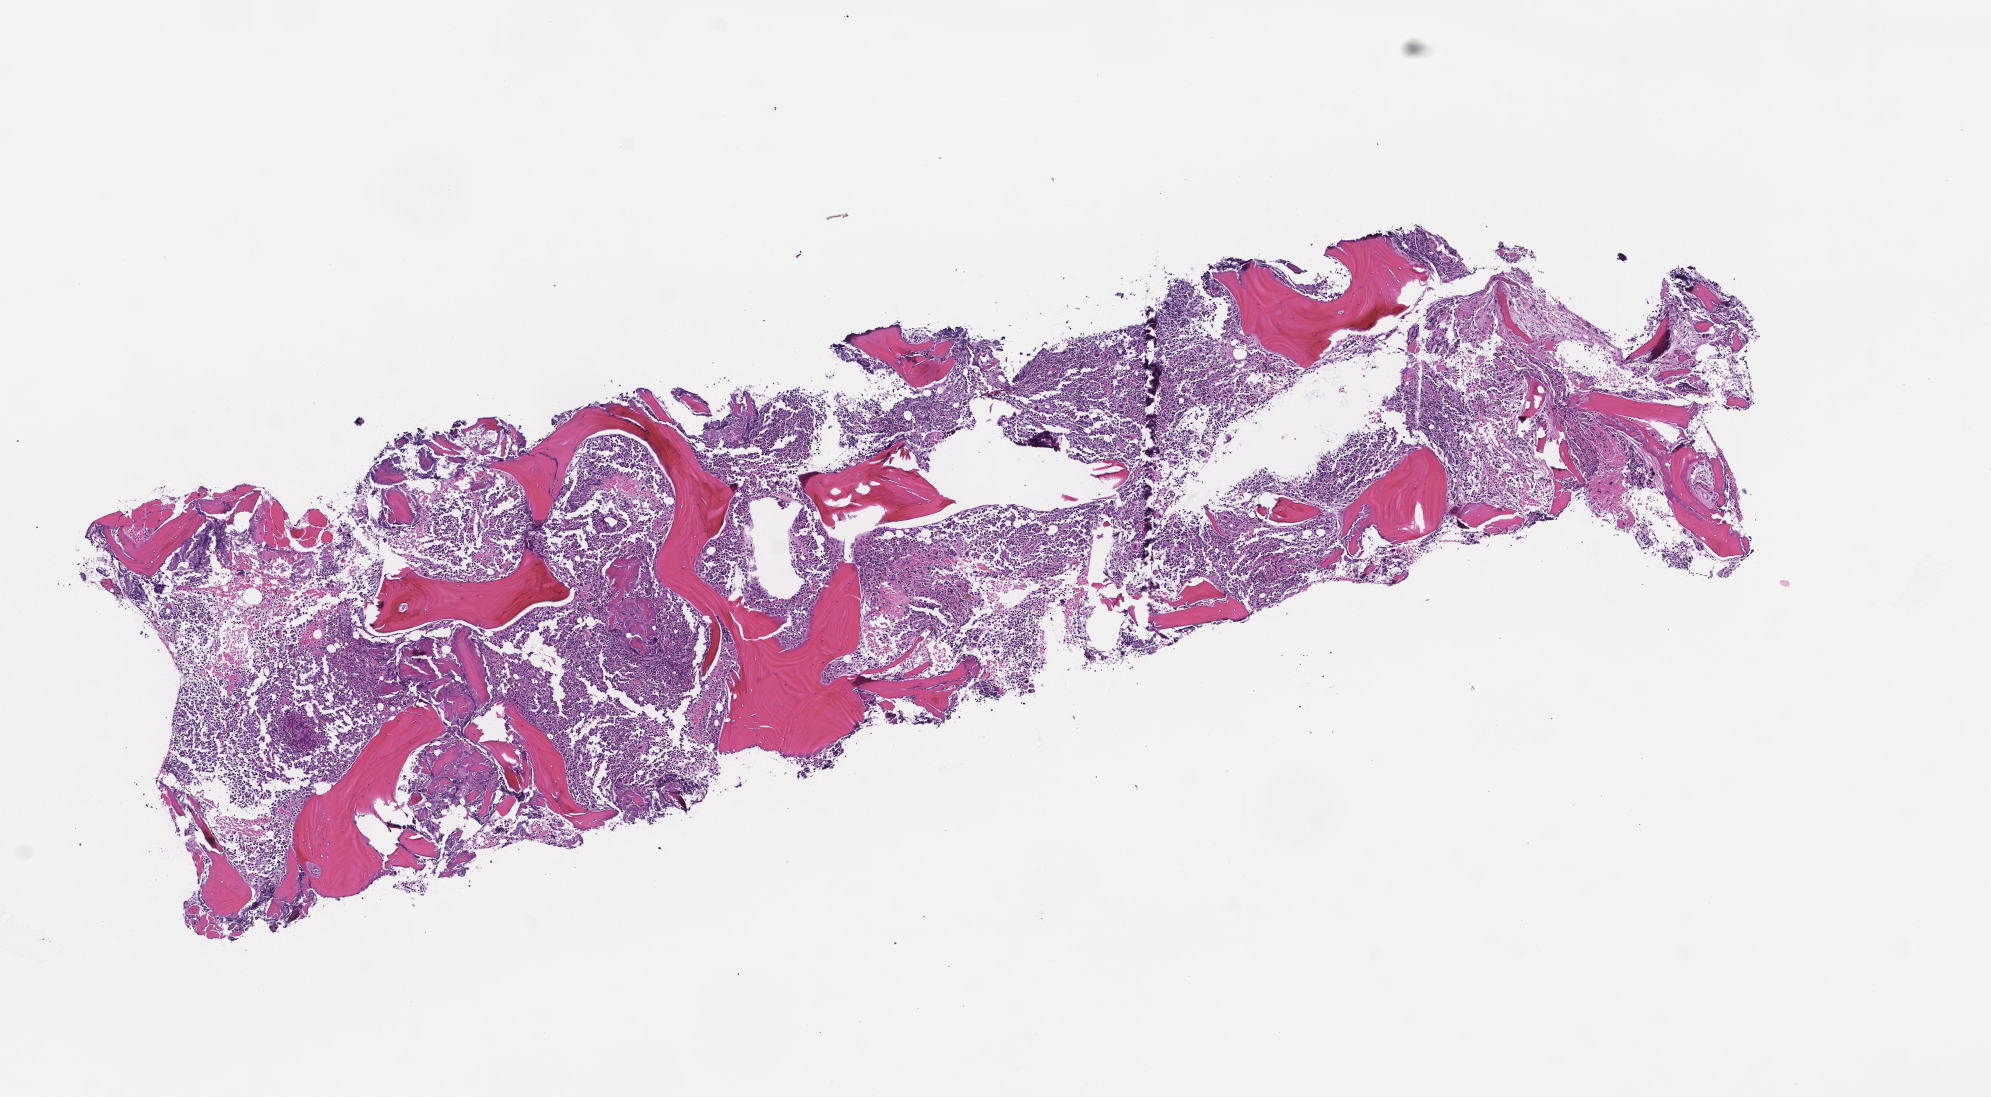
H&E whole-slide image, low-resolution overview of the scanned area, about 8.0 x 4.4 mm. Formalin-fixed paraffin-embedded section. Site: bone marrow. Patient: female.
Patient diagnosis: Acute Myeloid Leukemia Not Otherwise Specified.